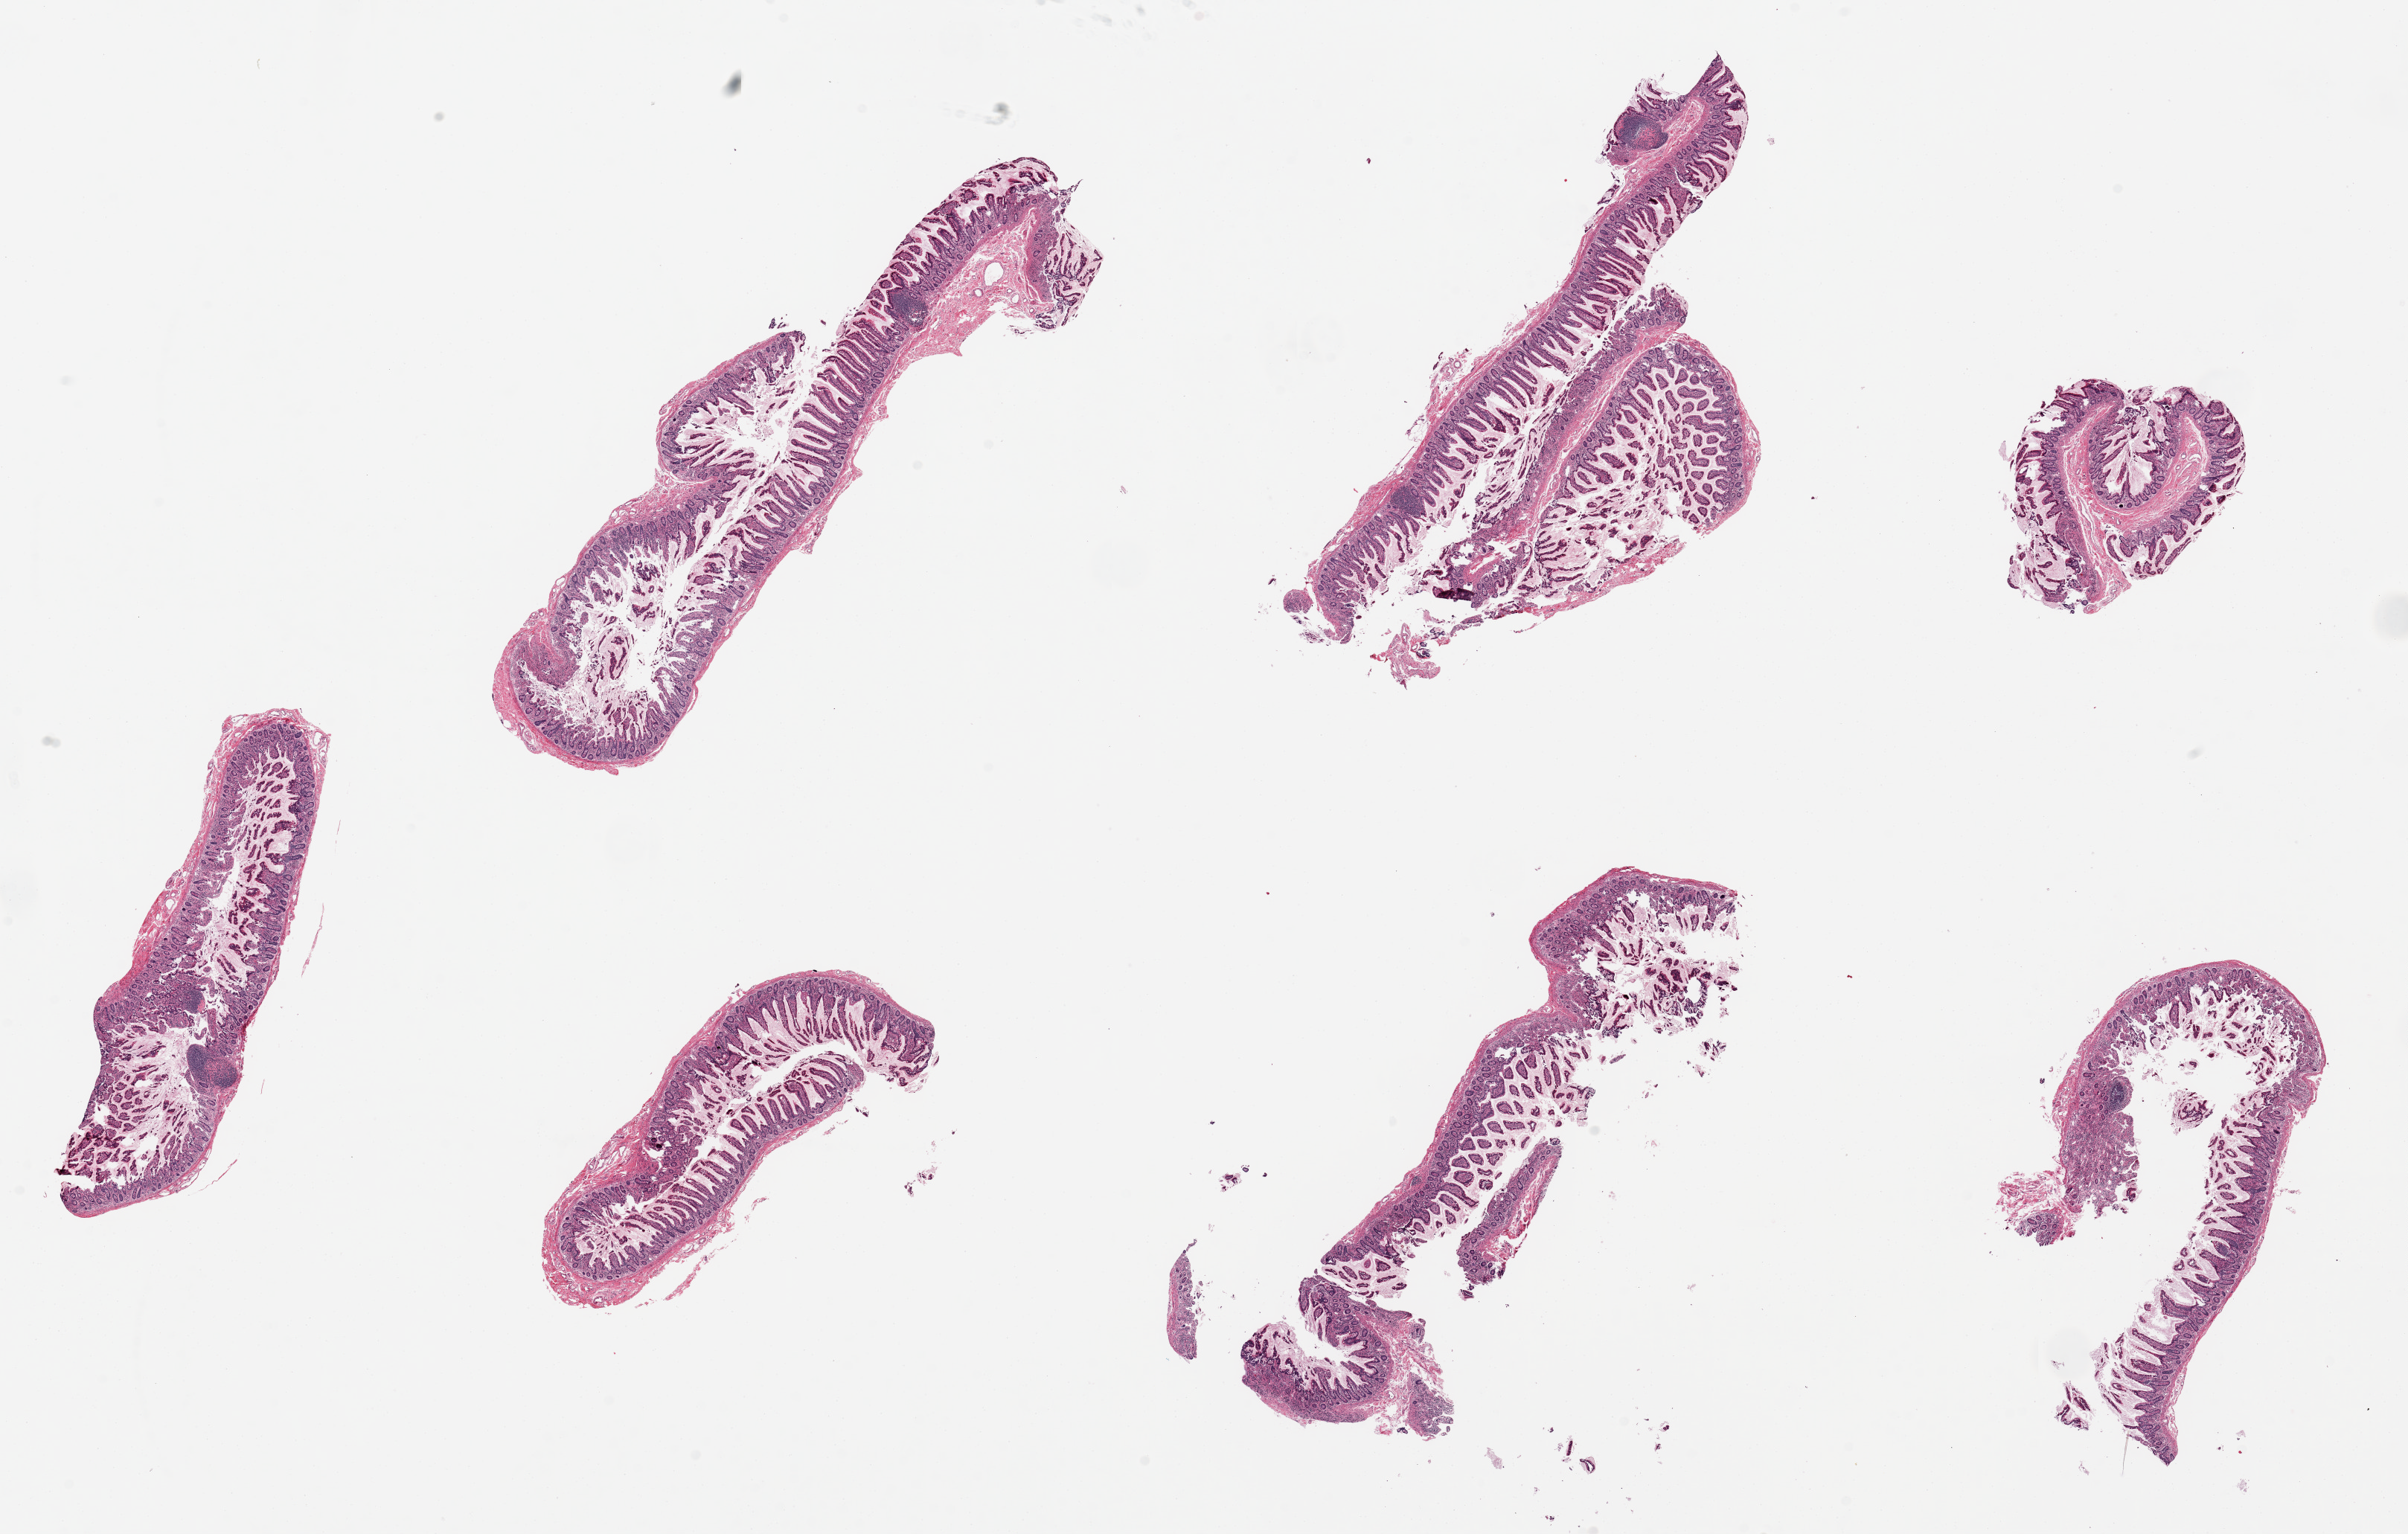
Digitized hematoxylin and eosin (H&E)-stained section, brightfield, whole scanned area (about 25.6 x 16.3 mm) shown as a low-resolution overview. PAXgene-fixed, paraffin-embedded tissue. Section of ileum (target tissue). Tissue donor sample. Female donor.
* reviewer comment on this tissue sample: 7 pieces, up to 8x3mm; rare lymphoid follicles mainly mucosa